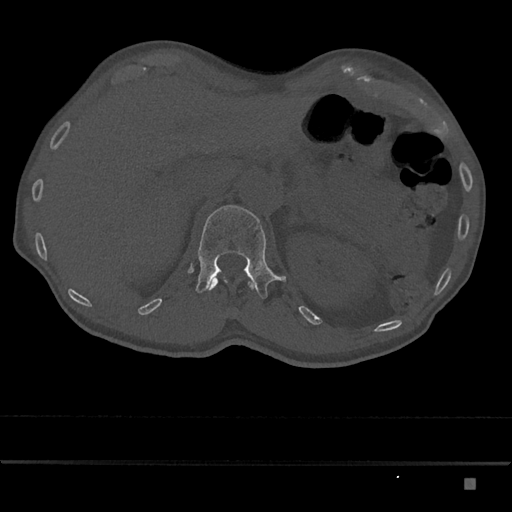
CT including the spine, one axial slice. Slice 565 of 797 in the series (ordered by position). Bone window (W 1800 / L 400 HU). 512 × 512 image matrix, field of view 390 × 390 mm. Male patient, age 72 years. Case-level facts recorded for this patient, not image findings: primary cancer: prostate.
Structures marked on this image (semi-automatic segmentation, software-assisted and operator-edited):
- L1 vertebra: bounding box [x1, y1, x2, y2] px = [196, 205, 286, 299]
- T12 vertebra: [206, 276, 256, 291]